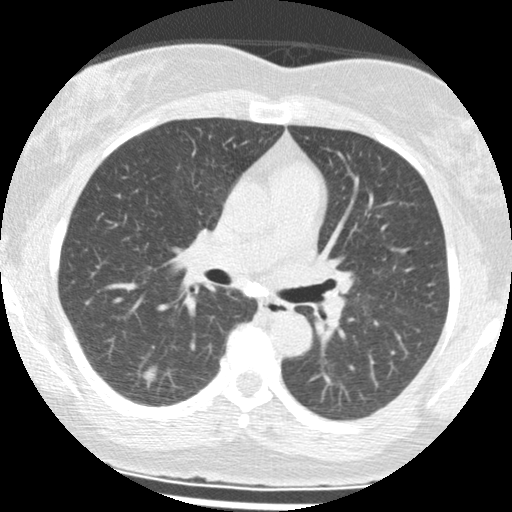
Chest CT (low-dose screening protocol), one axial image; first (baseline) screen; lung window (W 1500 / L -600 HU); 120 kVp; 512 × 512 image matrix, field of view 300 × 300 mm. Female participant, aged 65 years at enrolment. Current smoker at enrolment.
• Lesion marked by an expert reader, box from (x=129, y=358) to (x=166, y=392) px.
• Reader record for this screening exam (exam-level; its link to the box is not recorded): non-calcified nodule or mass ≥4 mm, right lower lobe, 8 × 6 mm, poorly defined margins, mixed attenuation.
• Official screen result: positive, change unspecified: nodule(s) >= 4 mm or enlarging nodule(s), mass(es), or other non-specific abnormalities suspicious for lung cancer.